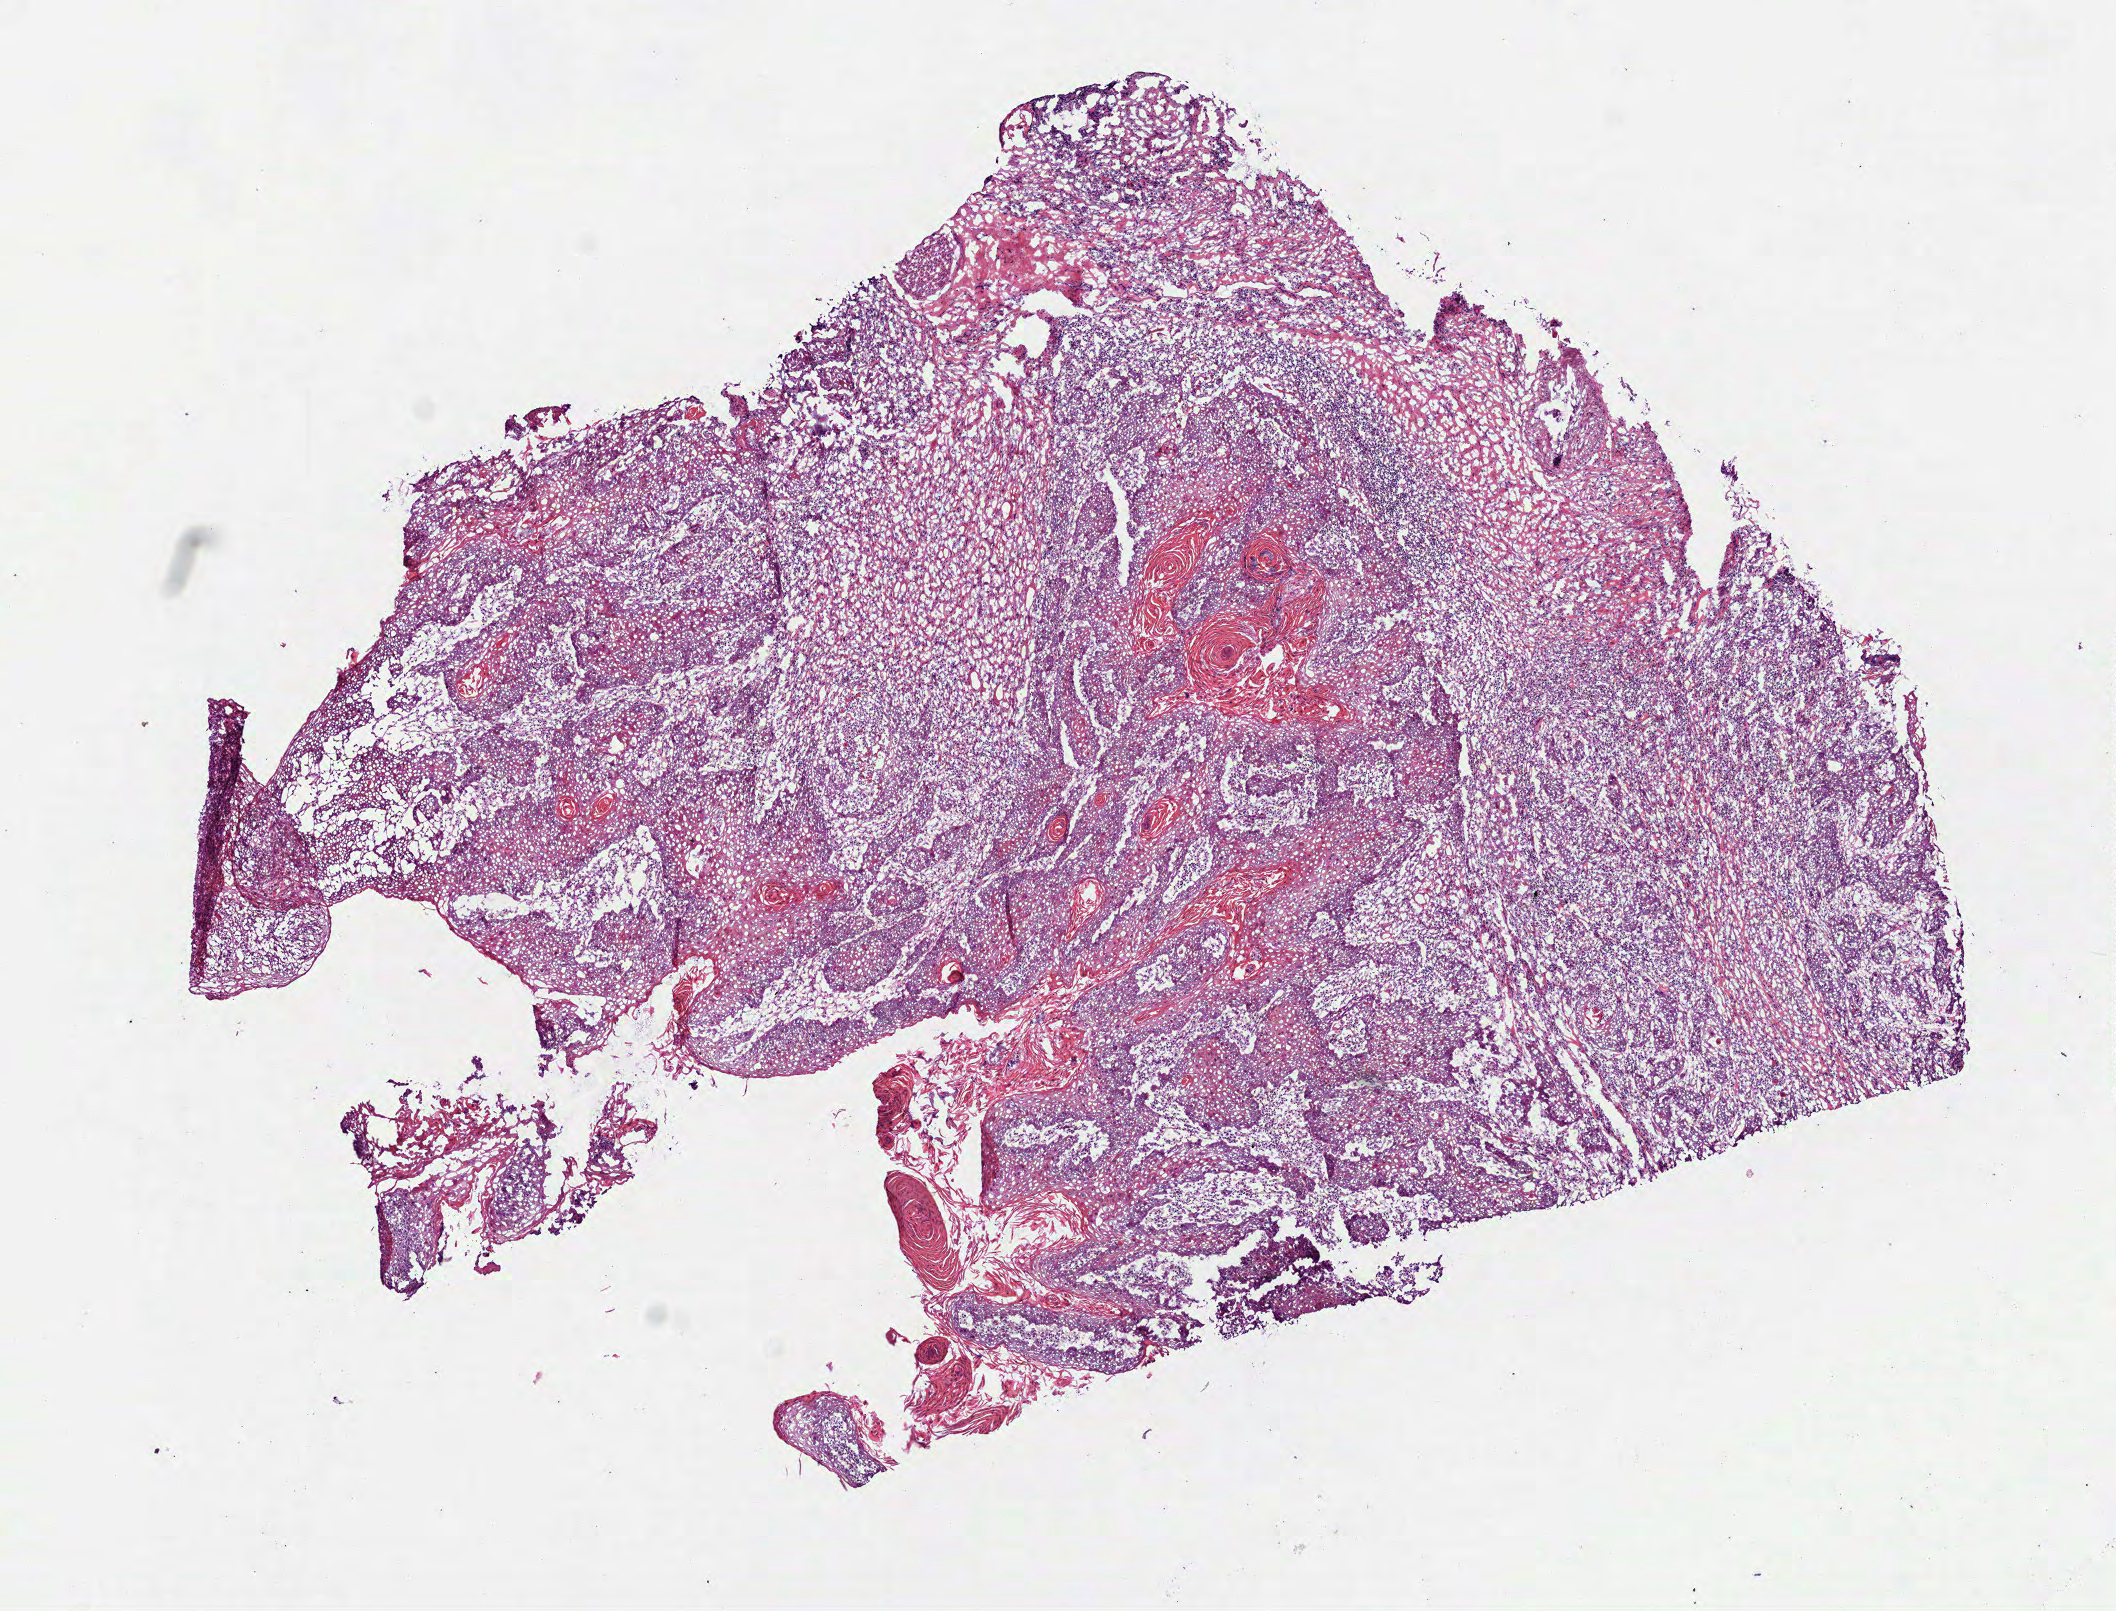
Whole-slide histology image, H&E-stained, a low-resolution overview of the entire scanned area, about 8.5 x 6.5 mm (acquisition: 40x scan), frozen section, head and neck, primary tumour sample. Male, age 69 years at initial diagnosis. Slide review estimates, as recorded: tumour cells 75%, tumour nuclei 70%.
Pathologic diagnosis: Squamous cell carcinoma, NOS.